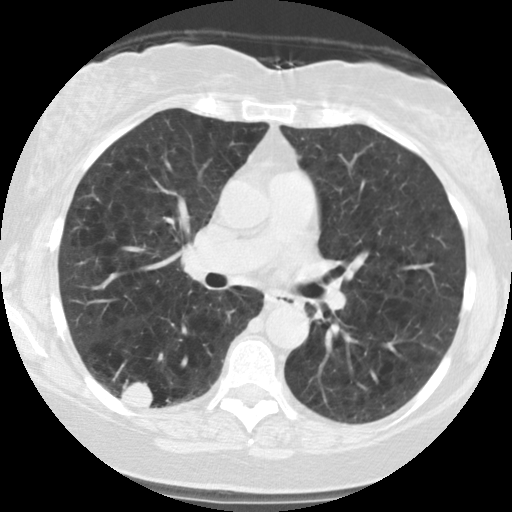
Axial slice from a low-dose chest CT screening exam. Second screening round (one year after baseline). Lung window (W 1500 / L -600 HU). Slice 58 of 122 in the series. Female, age 59 years at enrolment. Current smoker at enrolment.
• Expert-annotated lung lesion, box from (x=106, y=360) to (x=176, y=420) px.
• The screening reader recorded 2 non-calcified nodules or masses ≥4 mm on this exam (right lower lobe, right lower lobe); which of them this box marks is not recorded.
• Participant outcome: lung cancer diagnosed 63 days after this screen — squamous cell carcinoma, NOS, right lower lobe, poorly differentiated (G3), stage IB (AJCC 6th edition), 30 mm at pathology.